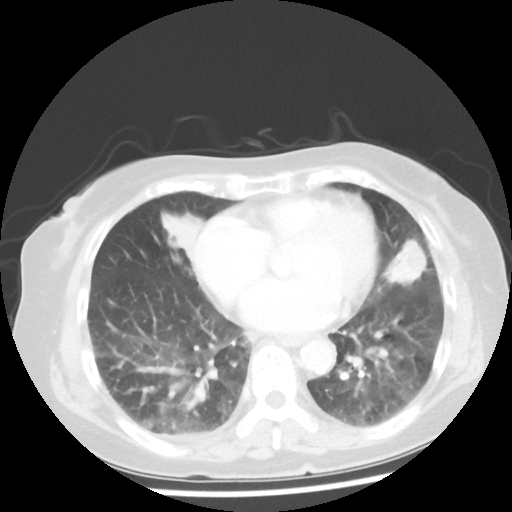
Chest CT, one axial slice. Slice 18 of 50 in the series (ordered by position). Reconstruction kernel STANDARD. 100 kVp. Lung window (W 1500 / L -600 HU). 5 mm slice thickness. 512 × 512 image matrix, field of view 332 × 332 mm. Female patient, age 77 years. Case-level facts recorded for this patient, not image findings: clinical TNM (as recorded): T2 N3 M1a.
Structures marked on this image (bounding box drawn by a radiologist):
- lung tumour (recorded histology: adenocarcinoma): box from (x=380, y=233) to (x=433, y=293) px